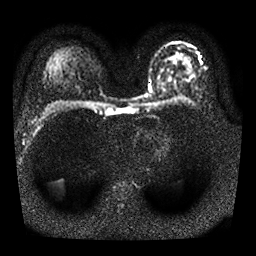
Breast MRI, one axial slice; slice 18 of 25 in the series (ordered by position); diffusion-weighted series; image 2 of 4 stored at this slice position (different b-values; order by instance number); 1.5 T; 256 × 256 image matrix. Female patient.
Annotated regions visible in this slice (outlined manually by an expert reader):
- tumour on diffusion-weighted imaging: bounding box <160,82,165,90> (left, top, right, bottom; pixels)